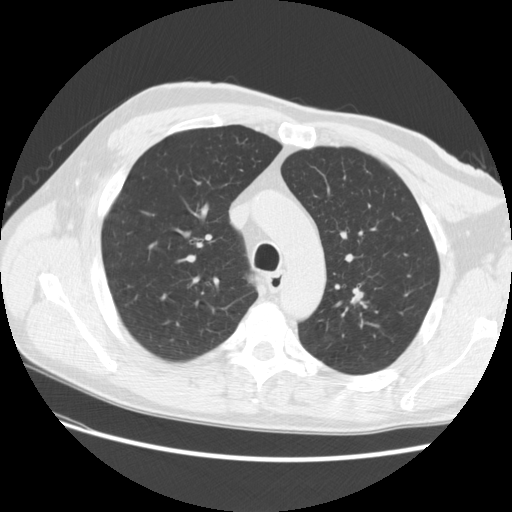
Low-dose screening chest CT, one axial slice. Position 188 of 256 along the scan axis. Reconstruction kernel STANDARD. 120 kVp. Lung window (W 1500 / L -600 HU). 512 × 512 image matrix, field of view 366 × 366 mm.
Structures marked on this image (expert manual segmentation):
- lesion 1 (tumor, upper lobe of left lung): bounding box (x1, y1, x2, y2) in pixels: (352, 292, 363, 303)